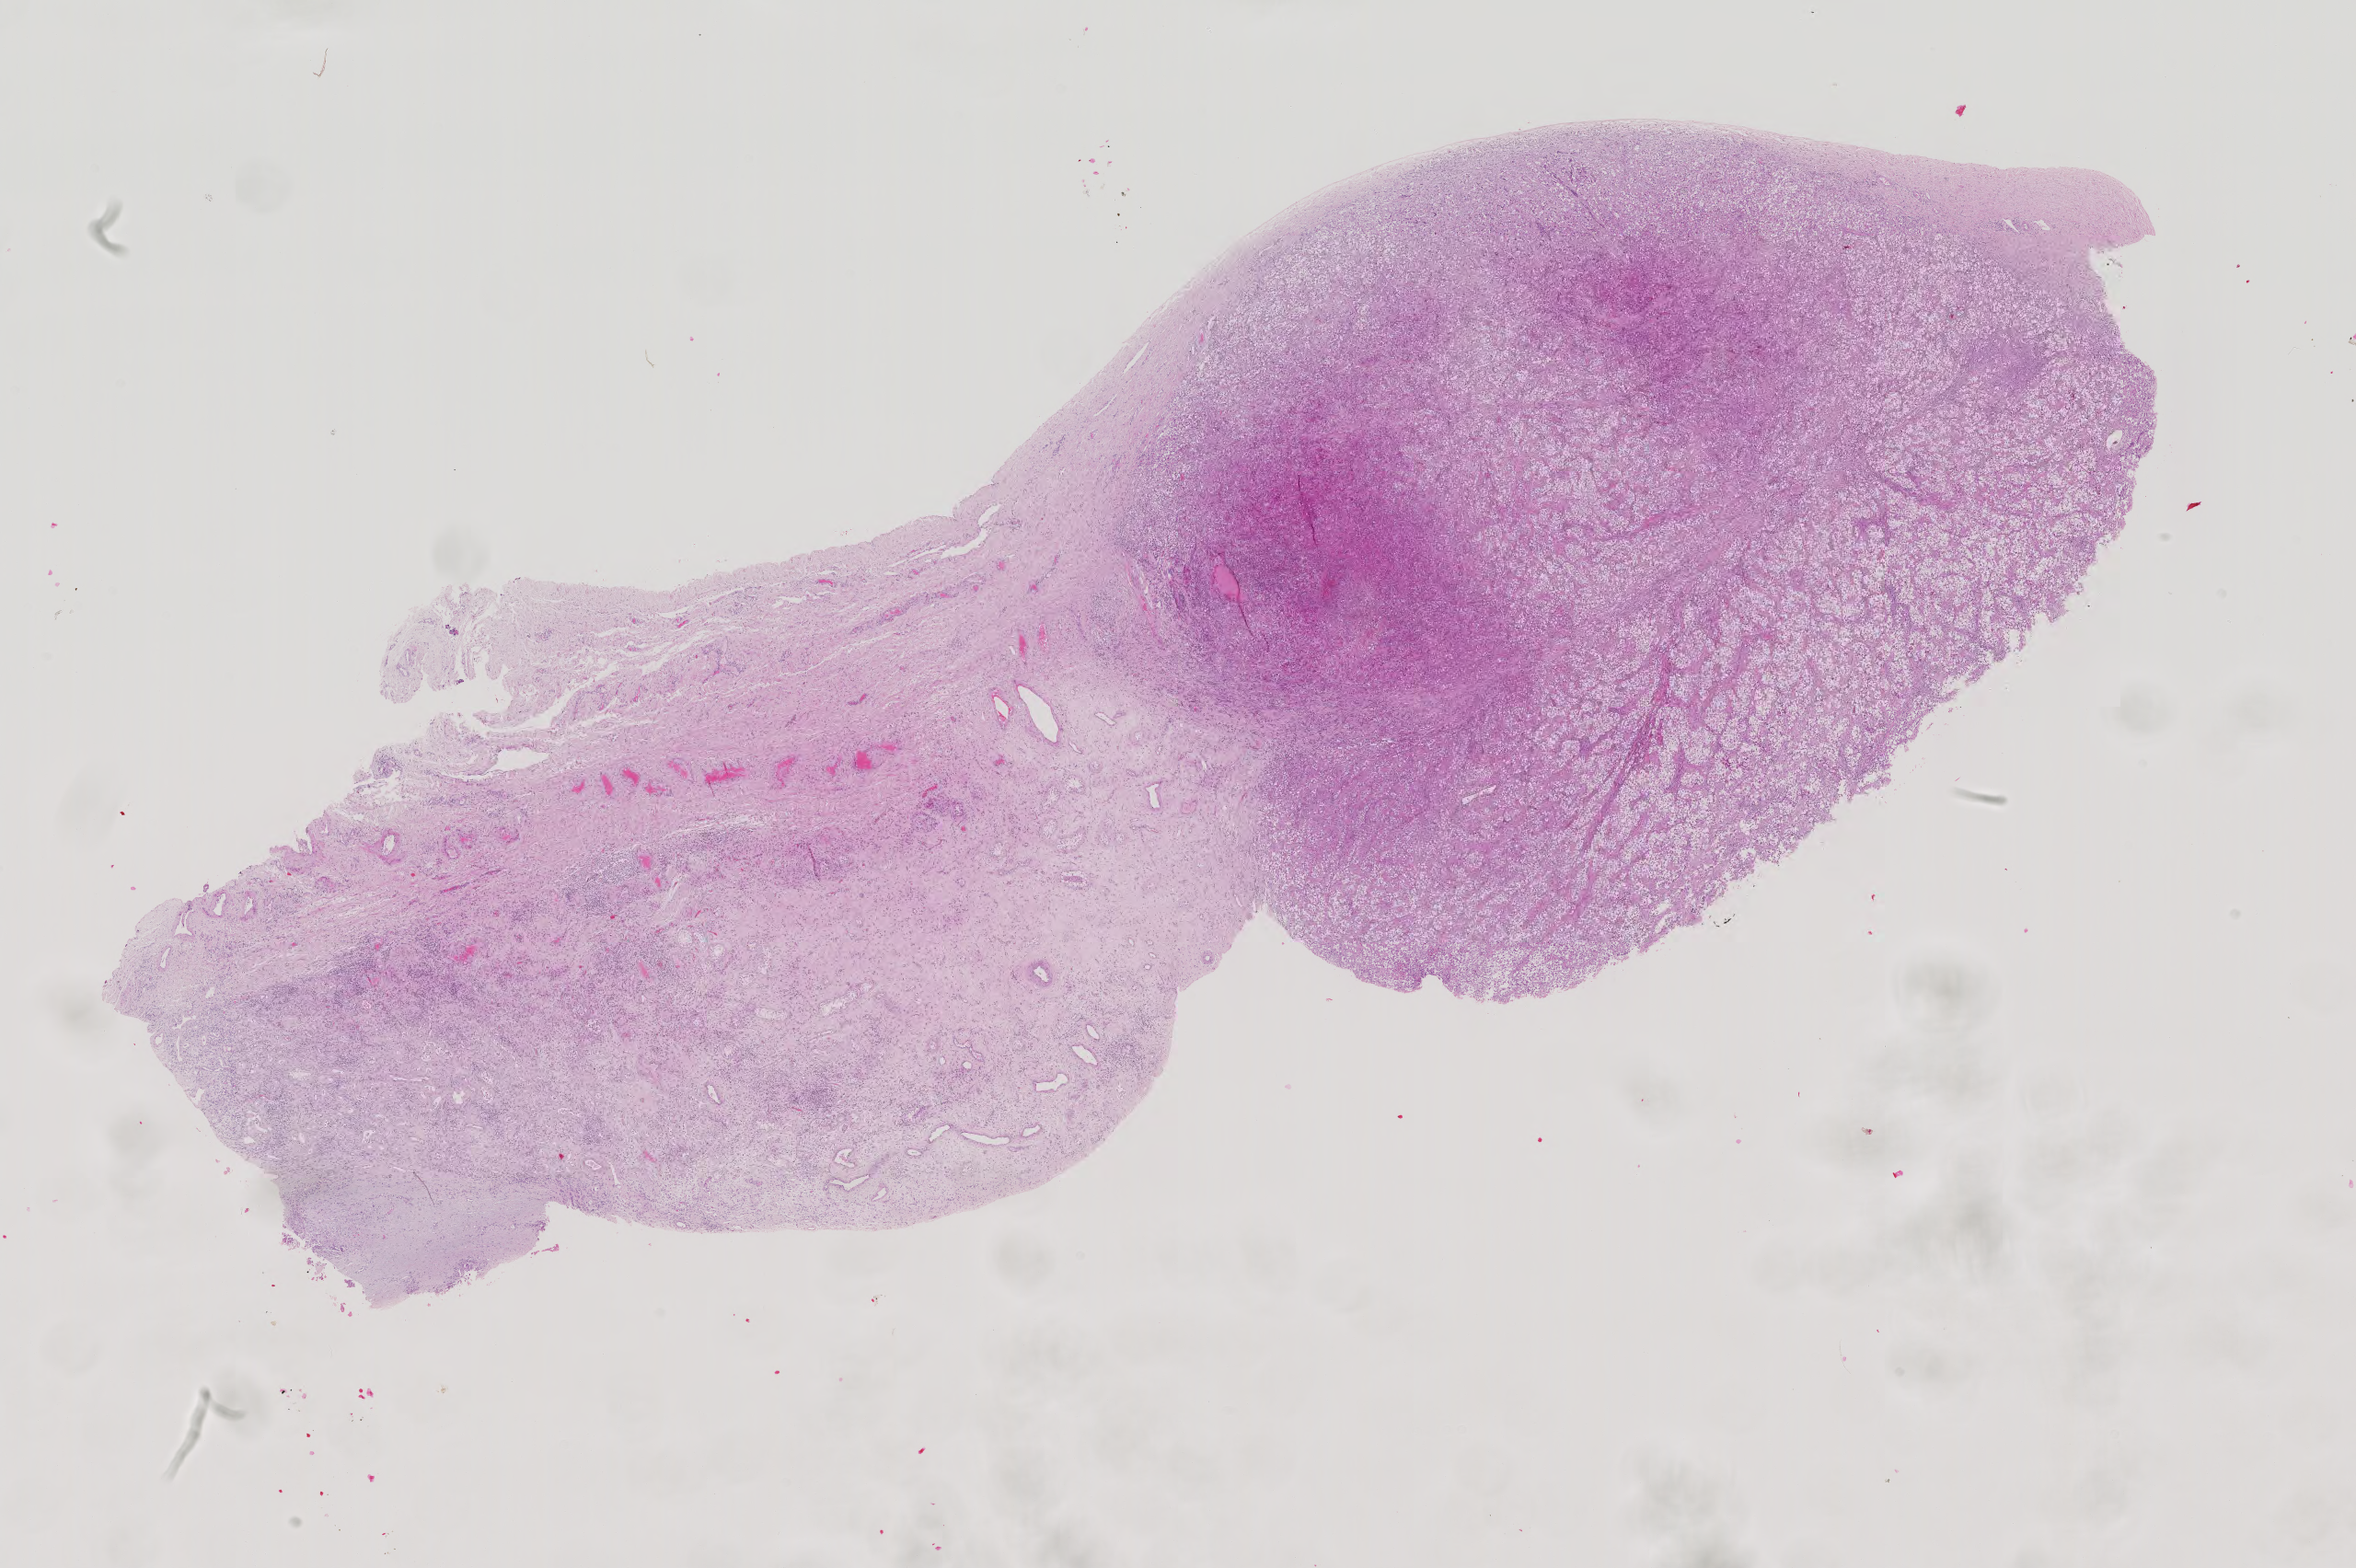
H&E-stained whole-slide image — low-resolution overview of the scanned area, about 18.7 x 12.4 mm (slide scanned at 40x); FFPE section; testis, primary tumour sample. Patient: male, age at initial diagnosis 27 years.
AJCC pathologic stage: IIIA. Pathologic diagnosis: Embryonal carcinoma, NOS.